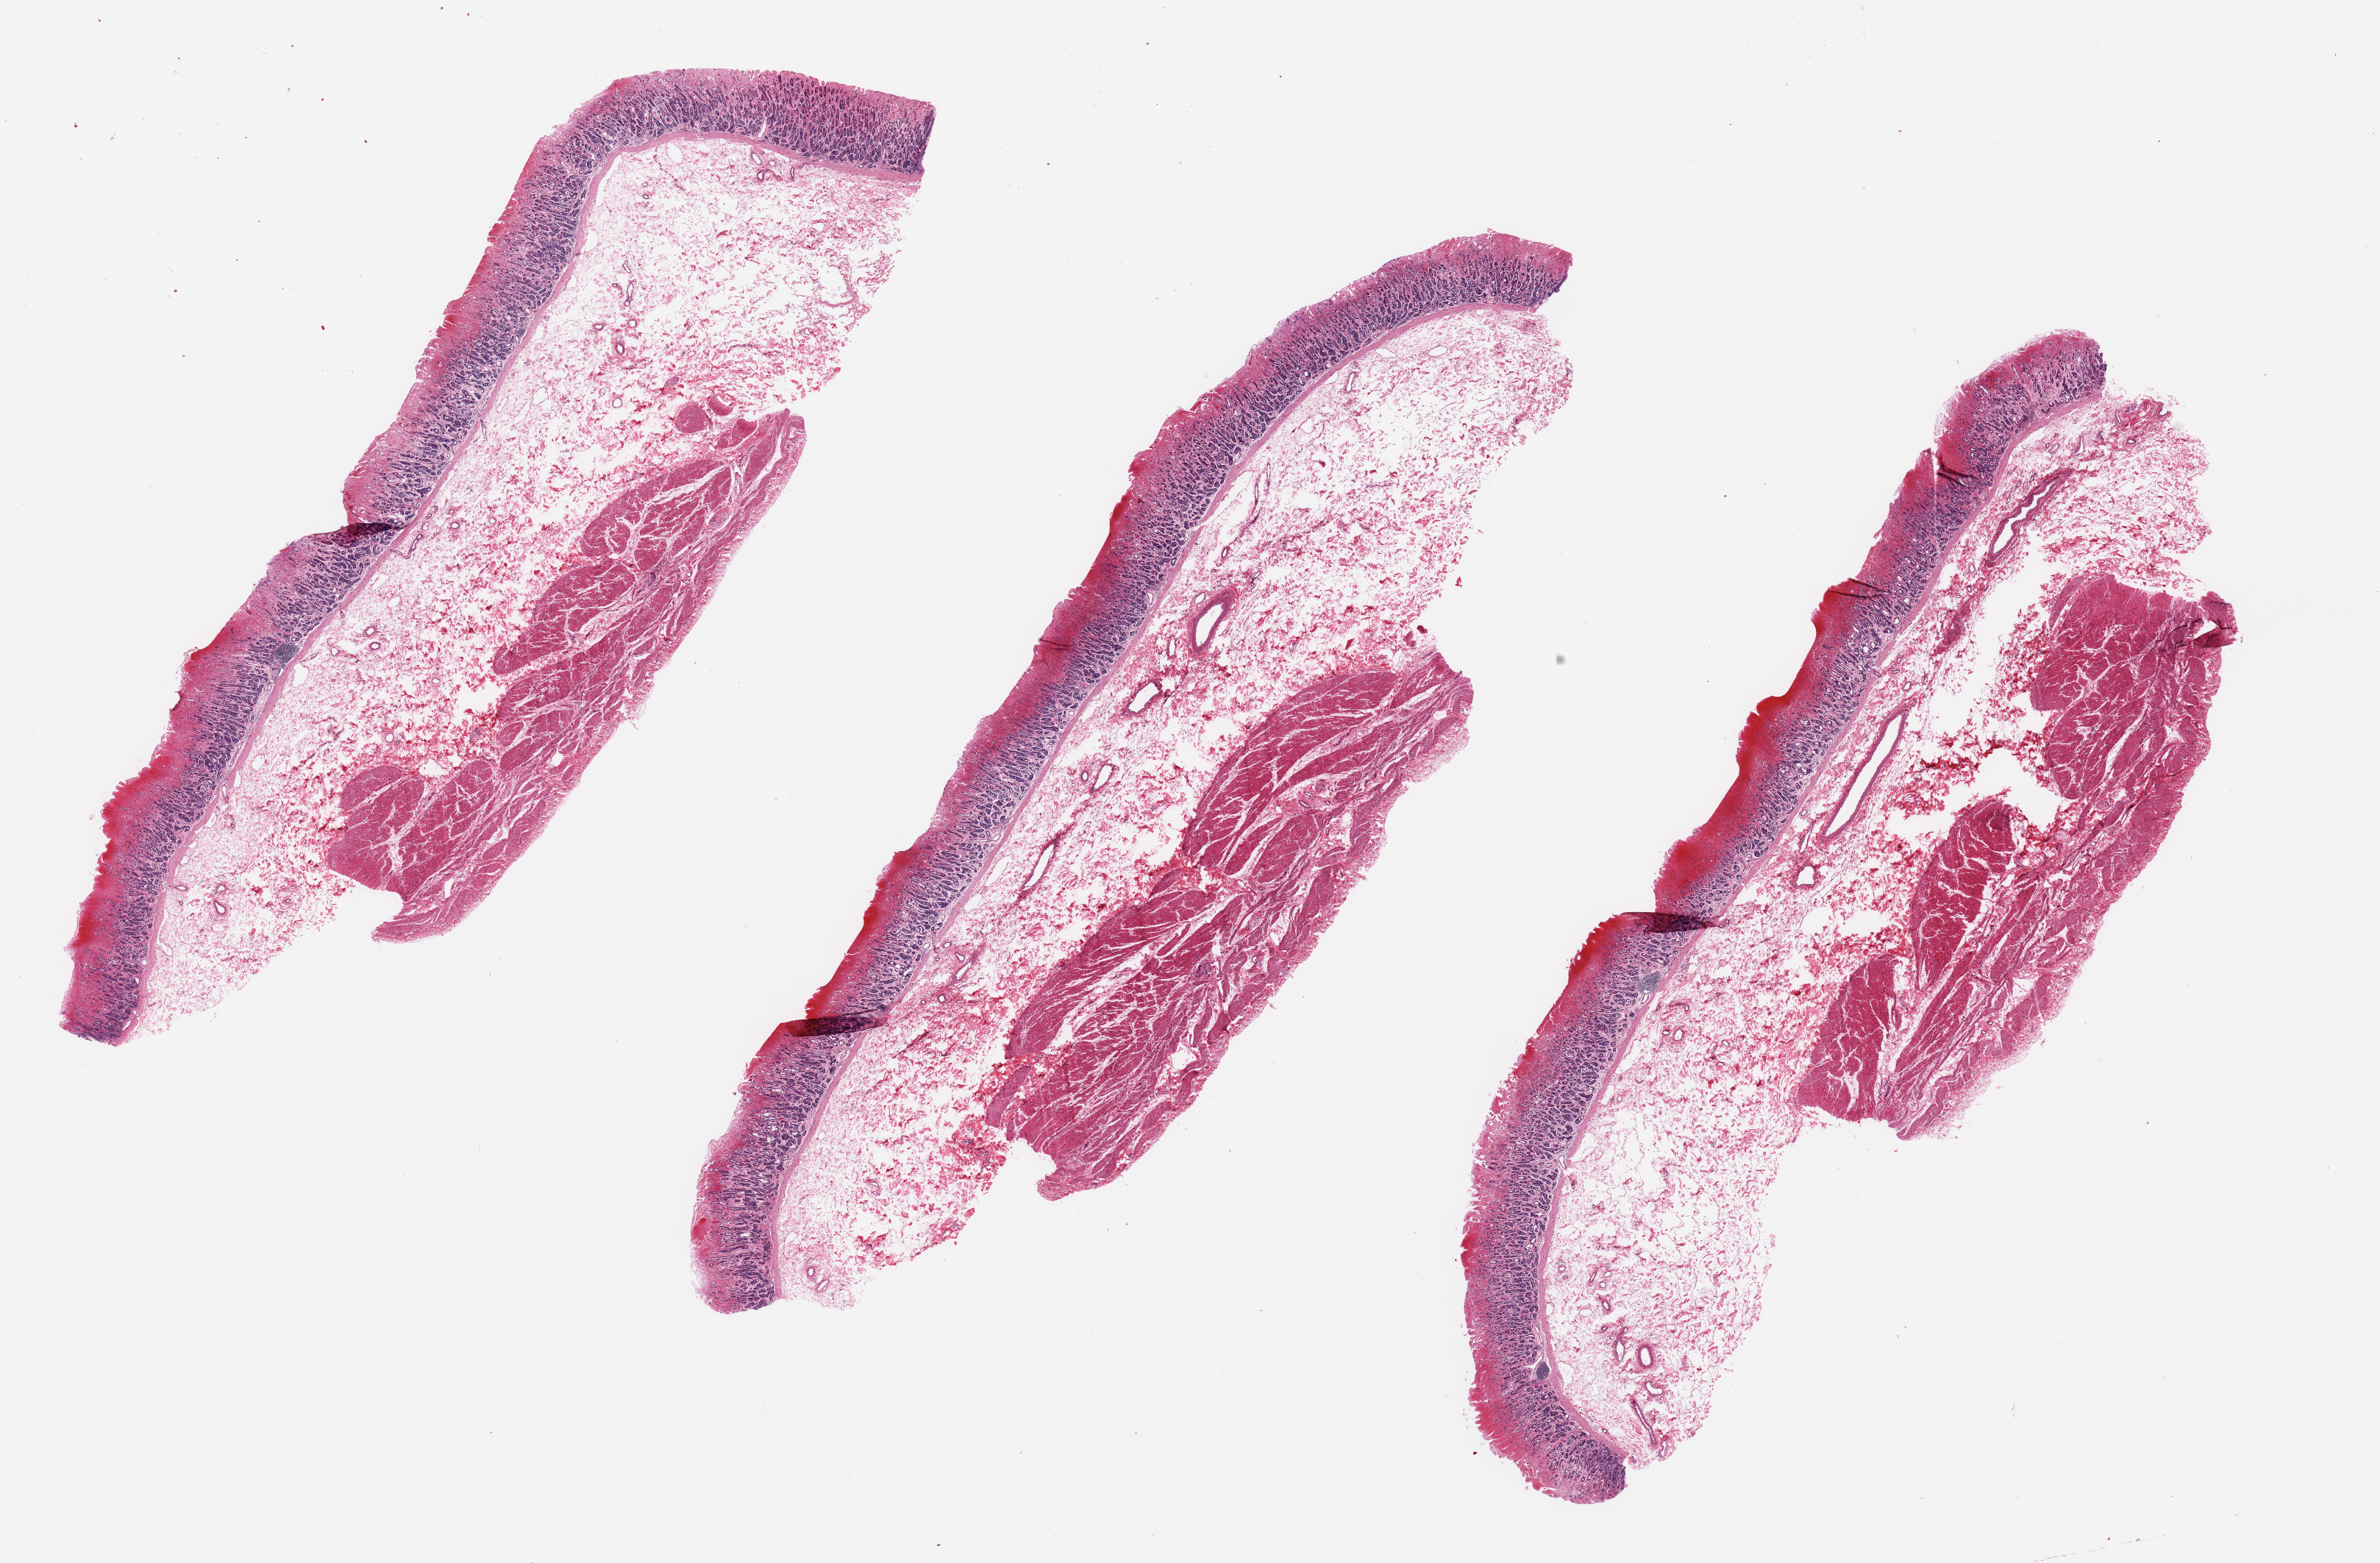
Hematoxylin and eosin (H&E) whole-slide image, brightfield — shown as a low-resolution overview of the whole scanned area (about 25.6 x 16.8 mm, slide scanned at 20x), PAXgene-fixed, paraffin-embedded tissue, target tissue: stomach, tissue donor sample. Donor sex: male.
Pathologist's review note for this sample: 50% mucosa is hemorrhagic.